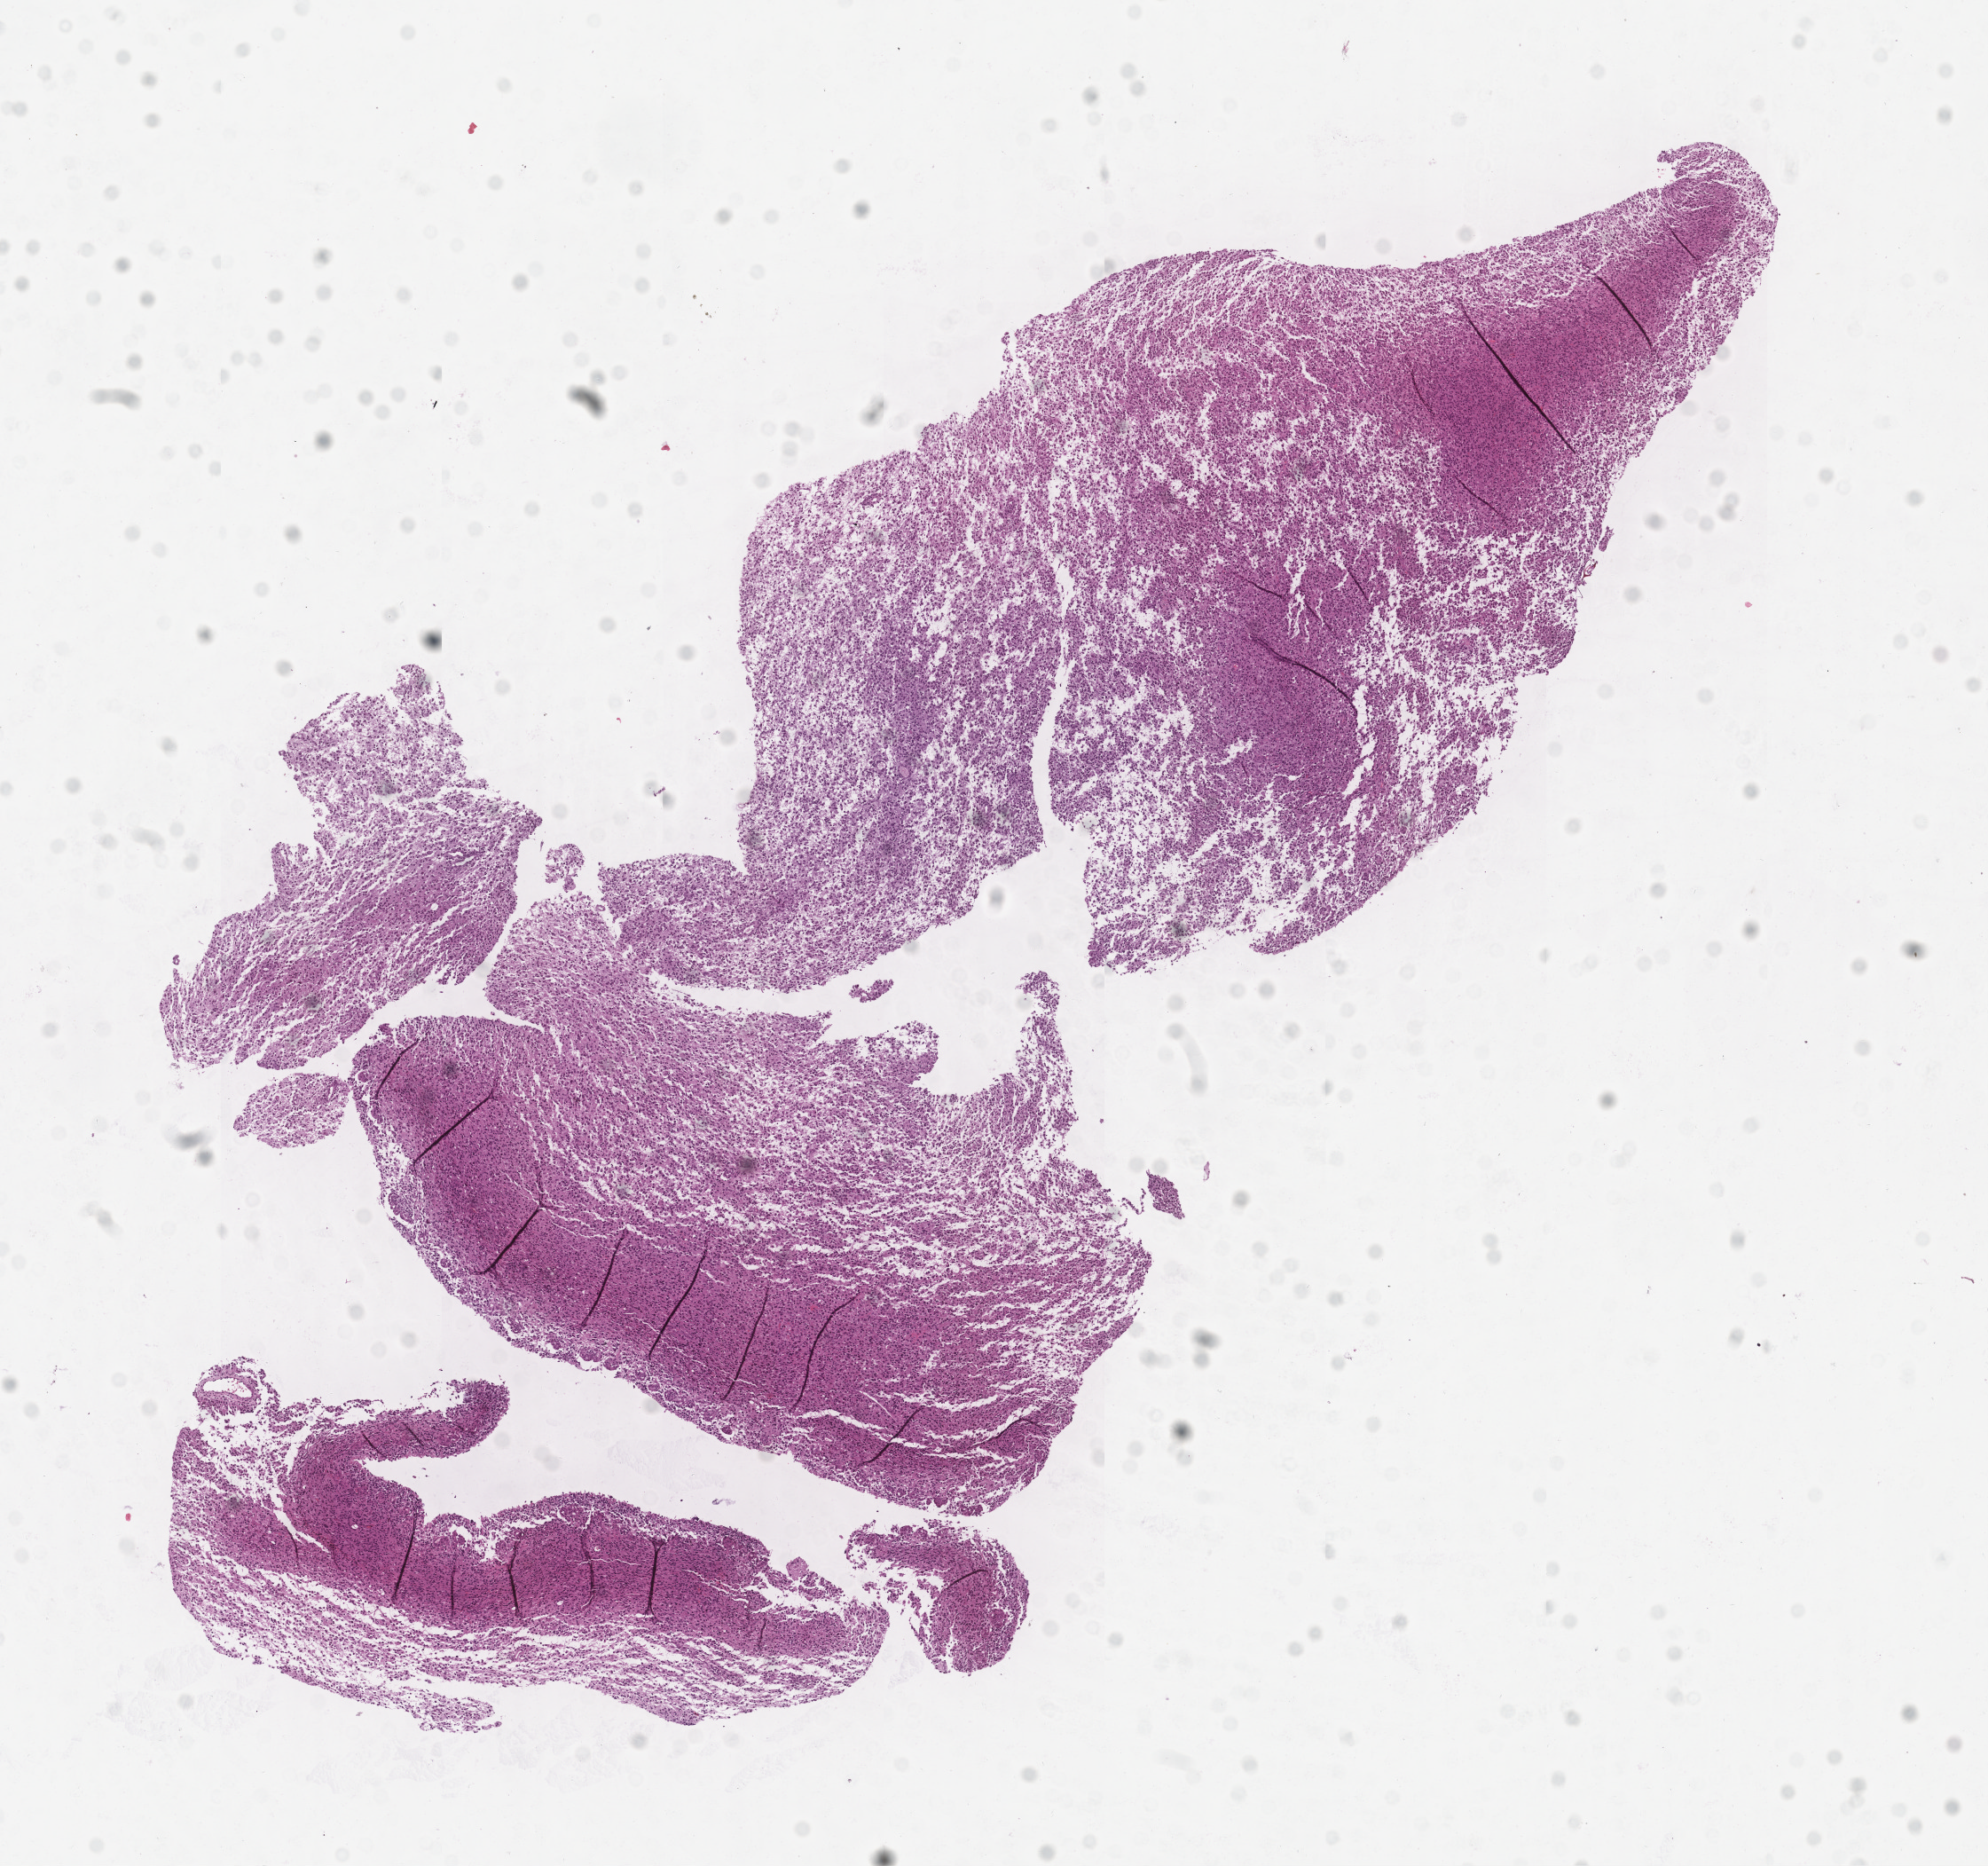
Hematoxylin and eosin (H&E) stained whole-slide image — a low-resolution overview of the entire scanned area, about 9.0 x 8.5 mm. Tumour tissue sample, sampled site: frontal lobe. 39-year-old male patient. Composition of this section per pathologist review: tumour nuclei 75%, necrosis 10%.
- primary tumour site (as recorded): frontal lobe
- diagnosis: Glioblastoma